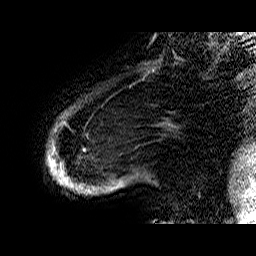
Breast MRI (dynamic contrast-enhanced), one sagittal slice. Slice 5 of 60 in the series (ordered by position). Dynamic contrast-enhanced series, time point 2 of 6 at this slice position (early post-contrast). 1.5 T. TE 6.4 ms, TR 32.9 ms. 256 × 256 image matrix, field of view 200 × 200 mm. Female patient. From the clinical record (not read from this slice): setting: breast cancer imaged before/during neoadjuvant chemotherapy; receptor status: HR-positive, HER2-negative.
Structures marked on this image (semi-automatic segmentation, software-assisted and operator-edited):
- analysis volume of interest (the breast-tissue region the enhancement analysis was run in; not a lesion): box from (x=47, y=100) to (x=149, y=195) px
- tumour enhancement mask (voxels above the 100 % enhancement threshold inside the analysis volume of interest): (x=48, y=123)–(x=68, y=184)